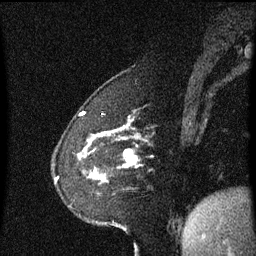
Breast MRI (dynamic contrast-enhanced), one sagittal slice. Slice 13 of 60 in the series (ordered by position). Dynamic contrast-enhanced series, image 2 of 3 at this slice position (ordered by acquisition). 1.5 T. TE 4.2 ms, TR 8.4 ms. 2.2 mm slice thickness. 256 × 256 image matrix, field of view 200 × 200 mm. Patient: female, 60 years. Case-level facts recorded for this patient, not image findings: setting: breast cancer imaged before/during neoadjuvant chemotherapy; receptor status: triple-negative.
Annotated regions visible in this slice (semi-automatically segmented with operator editing):
- analysis volume of interest (the breast-tissue region the enhancement analysis was run in; not a lesion): bounding box (x1, y1, x2, y2) in pixels: (79, 142, 136, 185)
- tumour enhancement mask (voxels above the 70 % enhancement threshold inside the analysis volume of interest): (125, 150, 135, 165)